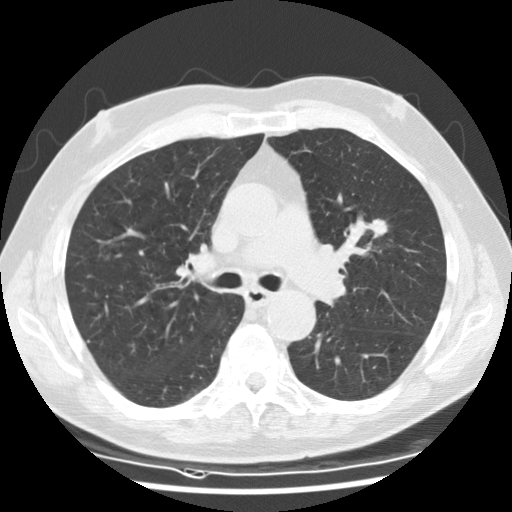
Axial slice from a low-dose chest CT screening exam; first (baseline) screen; lung window (W 1500 / L -600 HU); 2.5 mm slice thickness; standard (soft-tissue) reconstruction kernel (STANDARD); slice 57 of 135 in the series. Male participant, aged 73 years at enrolment.
• Lesion marked by an expert reader, bounding box (x1, y1, x2, y2) in pixels: (347, 202, 407, 255).
• The exam's reader record, not a measurement of the box and not confirmed to be the same lesion: non-calcified nodule or mass ≥4 mm, right lower lobe, 13 × 13 mm, smooth margins, soft tissue attenuation.
• Note: the box lies in the patient's left hemithorax on this image, whereas the reader's record names the right lung; they may be different findings.
• Lung cancer was diagnosed 307 days after this screen: adenocarcinoma, NOS, left upper lobe, poorly differentiated (G3), stage IA (AJCC 6th edition), 19 mm at pathology.